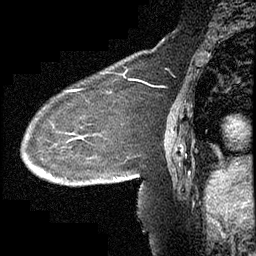
Breast MRI (dynamic contrast-enhanced), one sagittal slice; slice 146 of 232 in the series (ordered by position); dynamic contrast-enhanced study with each time point stored as its own series, time point 2 of 4 at this slice position (early post-contrast, ordered by acquisition time); 1.5 T; TE 4.2 ms, TR 6.7 ms; 256 × 256 image matrix, field of view 200 × 200 mm. Female patient, age 63 years. Case-level facts recorded for this patient, not image findings: setting: breast cancer imaged before/during neoadjuvant chemotherapy; receptor status: triple-negative.
Annotated regions visible in this slice (semi-automatically segmented with operator editing):
- analysis volume of interest (the breast-tissue region the enhancement analysis was run in; not a lesion): bounding box [x1, y1, x2, y2] px = [21, 90, 140, 211]
- tumour enhancement mask (voxels above the 70 % enhancement threshold inside the analysis volume of interest): [67, 90, 116, 180]